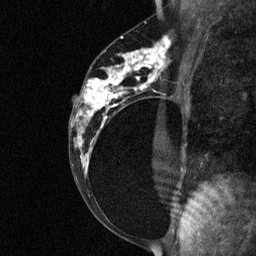
Breast MRI (dynamic contrast-enhanced), one sagittal slice; slice 36 of 64 in the series (ordered by position); dynamic contrast-enhanced study with each time point stored as its own series, time point 2 of 3 at this slice position (early post-contrast, ordered by acquisition time); 1.5 T; TE 4.8 ms, TR 27 ms; 2 mm slice thickness; 256 × 256 image matrix, field of view 180 × 180 mm. Patient: female, 34 years. From the clinical record (not read from this slice): setting: breast cancer imaged before/during neoadjuvant chemotherapy; receptor status: HR-positive, HER2-negative.
Annotated regions visible in this slice (semi-automatically segmented with operator editing):
- analysis volume of interest (the breast-tissue region the enhancement analysis was run in; not a lesion): bounding box (x1, y1, x2, y2) in pixels: (78, 44, 181, 191)
- tumour enhancement mask (voxels above the 90 % enhancement threshold inside the analysis volume of interest): (81, 44, 169, 167)